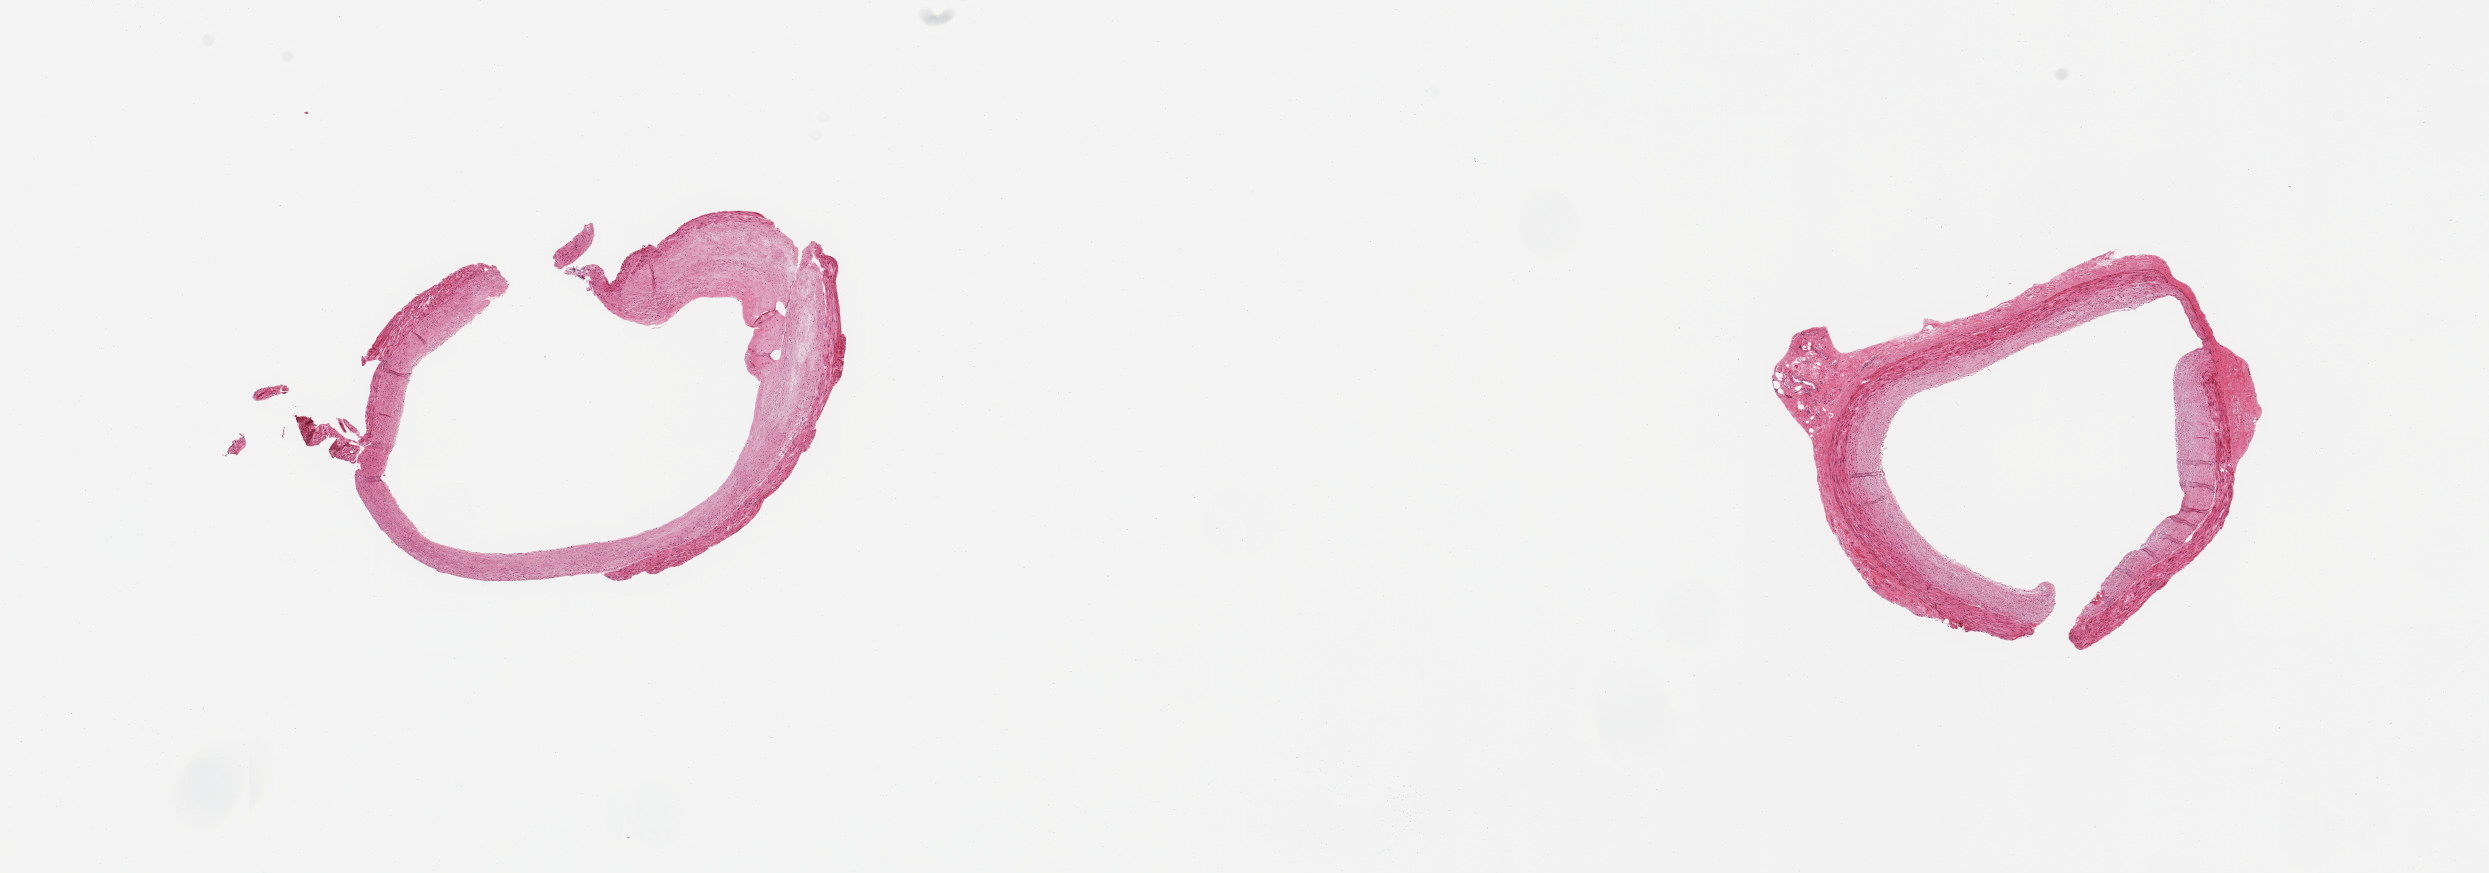
Digitized hematoxylin and eosin (H&E)-stained section, low-resolution overview of the scanned area, about 19.7 x 6.9 mm (slide scanned at 20x), PAXgene-fixed paraffin-embedded (PFPE) section, target tissue: coronary artery, donor tissue sample.
Reviewer comment on this tissue sample: 2 pieces; interrupted vessel wall with fibrosclerotic plaque; up to 0.8 mm attached adventitia.